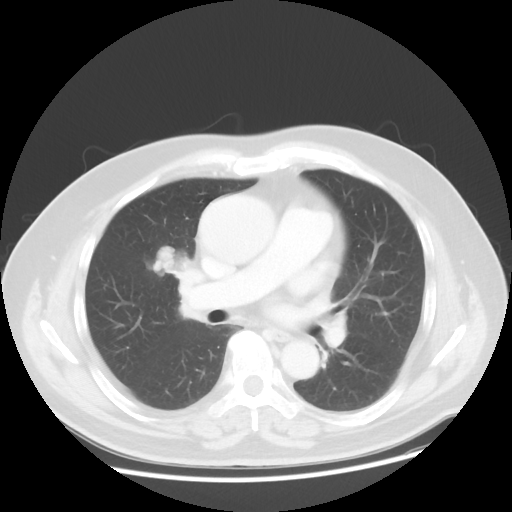
Chest CT, one axial slice. Slice 25 of 48 in the series (ordered by position). 120 kVp. Lung window (W 1500 / L -600 HU). 5 mm slice thickness. 512 × 512 image matrix, field of view 392 × 392 mm. Patient: male, 60 years. From the clinical record (not read from this slice): clinical TNM (as recorded): T2 N3 M0; histopathological grade: G2-3.
Outlined on this slice (bounding box drawn by a radiologist):
- lung tumour (recorded histology: adenocarcinoma): bounding box (x1, y1, x2, y2) in pixels: (145, 233, 192, 285)